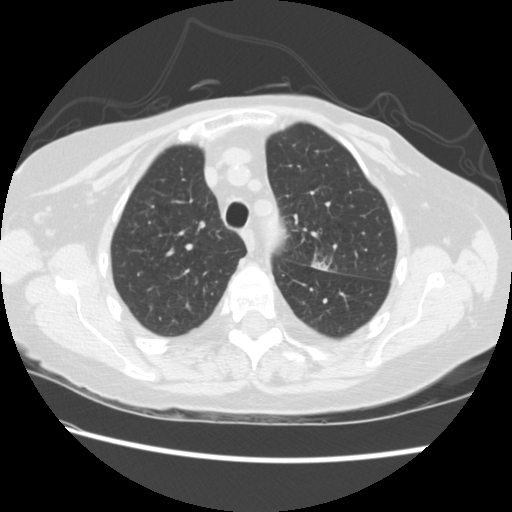
Low-dose screening chest CT, axial slice. Baseline screening round. Lung window (W 1500 / L -600 HU). 2.5 mm slice thickness. 120 kVp. Slice 60 of 224 in the series. Female, age 74 years at enrolment.
Expert reader's lesion annotation, bounding box (x1, y1, x2, y2) in pixels: (296, 234, 346, 279). The screening reader recorded 2 non-calcified nodules or masses ≥4 mm on this exam (left upper lobe, right lower lobe); which of them this box marks is not recorded. Lung cancer was diagnosed 309 days after this screen: non-small cell carcinoma, left upper lobe, stage IV (AJCC 6th edition).